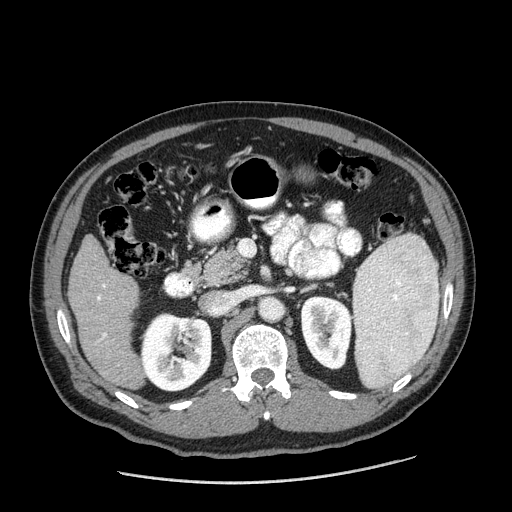
Contrast-enhanced abdominal CT (liver protocol), one axial slice. Slice 77 of 198 in the series (ordered by position). Reconstruction kernel STANDARD. 120 kVp. One of 2 acquisitions stored at this slice position. Soft-tissue window (W 400 / L 40 HU). 512 × 512 image matrix, field of view 400 × 400 mm. From the clinical record (not read from this slice): diagnosis: hepatocellular carcinoma (patient treated with transarterial chemoembolisation; whether this scan precedes or follows treatment is not stated here); TNM stage (as recorded): Stage-II; Child-Pugh class: A; tumour differentiation: moderately differentiated; tumour nodularity: multinodular.
Structures marked on this image (semi-automatic segmentation, software-assisted and operator-edited):
- liver parenchyma outside the tumour (the mass and vessels are separate outlines, so this box may not span the whole liver): bounding box (x1, y1, x2, y2) in pixels: (68, 234, 144, 388)
- liver vessels: (97, 284, 107, 340)